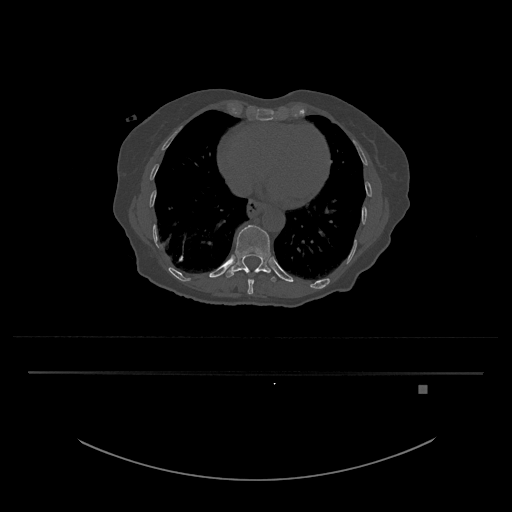
CT including the spine, one axial slice; slice 681 of 797 in the series (ordered by position); reconstruction kernel Br40s/3; 120 kVp; bone window (W 1800 / L 400 HU); 0.5 mm slice thickness; 512 × 512 image matrix, field of view 500 × 500 mm. Patient: female, 57 years. Case-level facts recorded for this patient, not image findings: primary cancer: cervical.
Outlined on this slice (semi-automatically segmented with operator editing):
- T10 vertebra: bounding box [x1, y1, x2, y2] px = [247, 271, 254, 295]
- T11 vertebra: [225, 225, 277, 282]